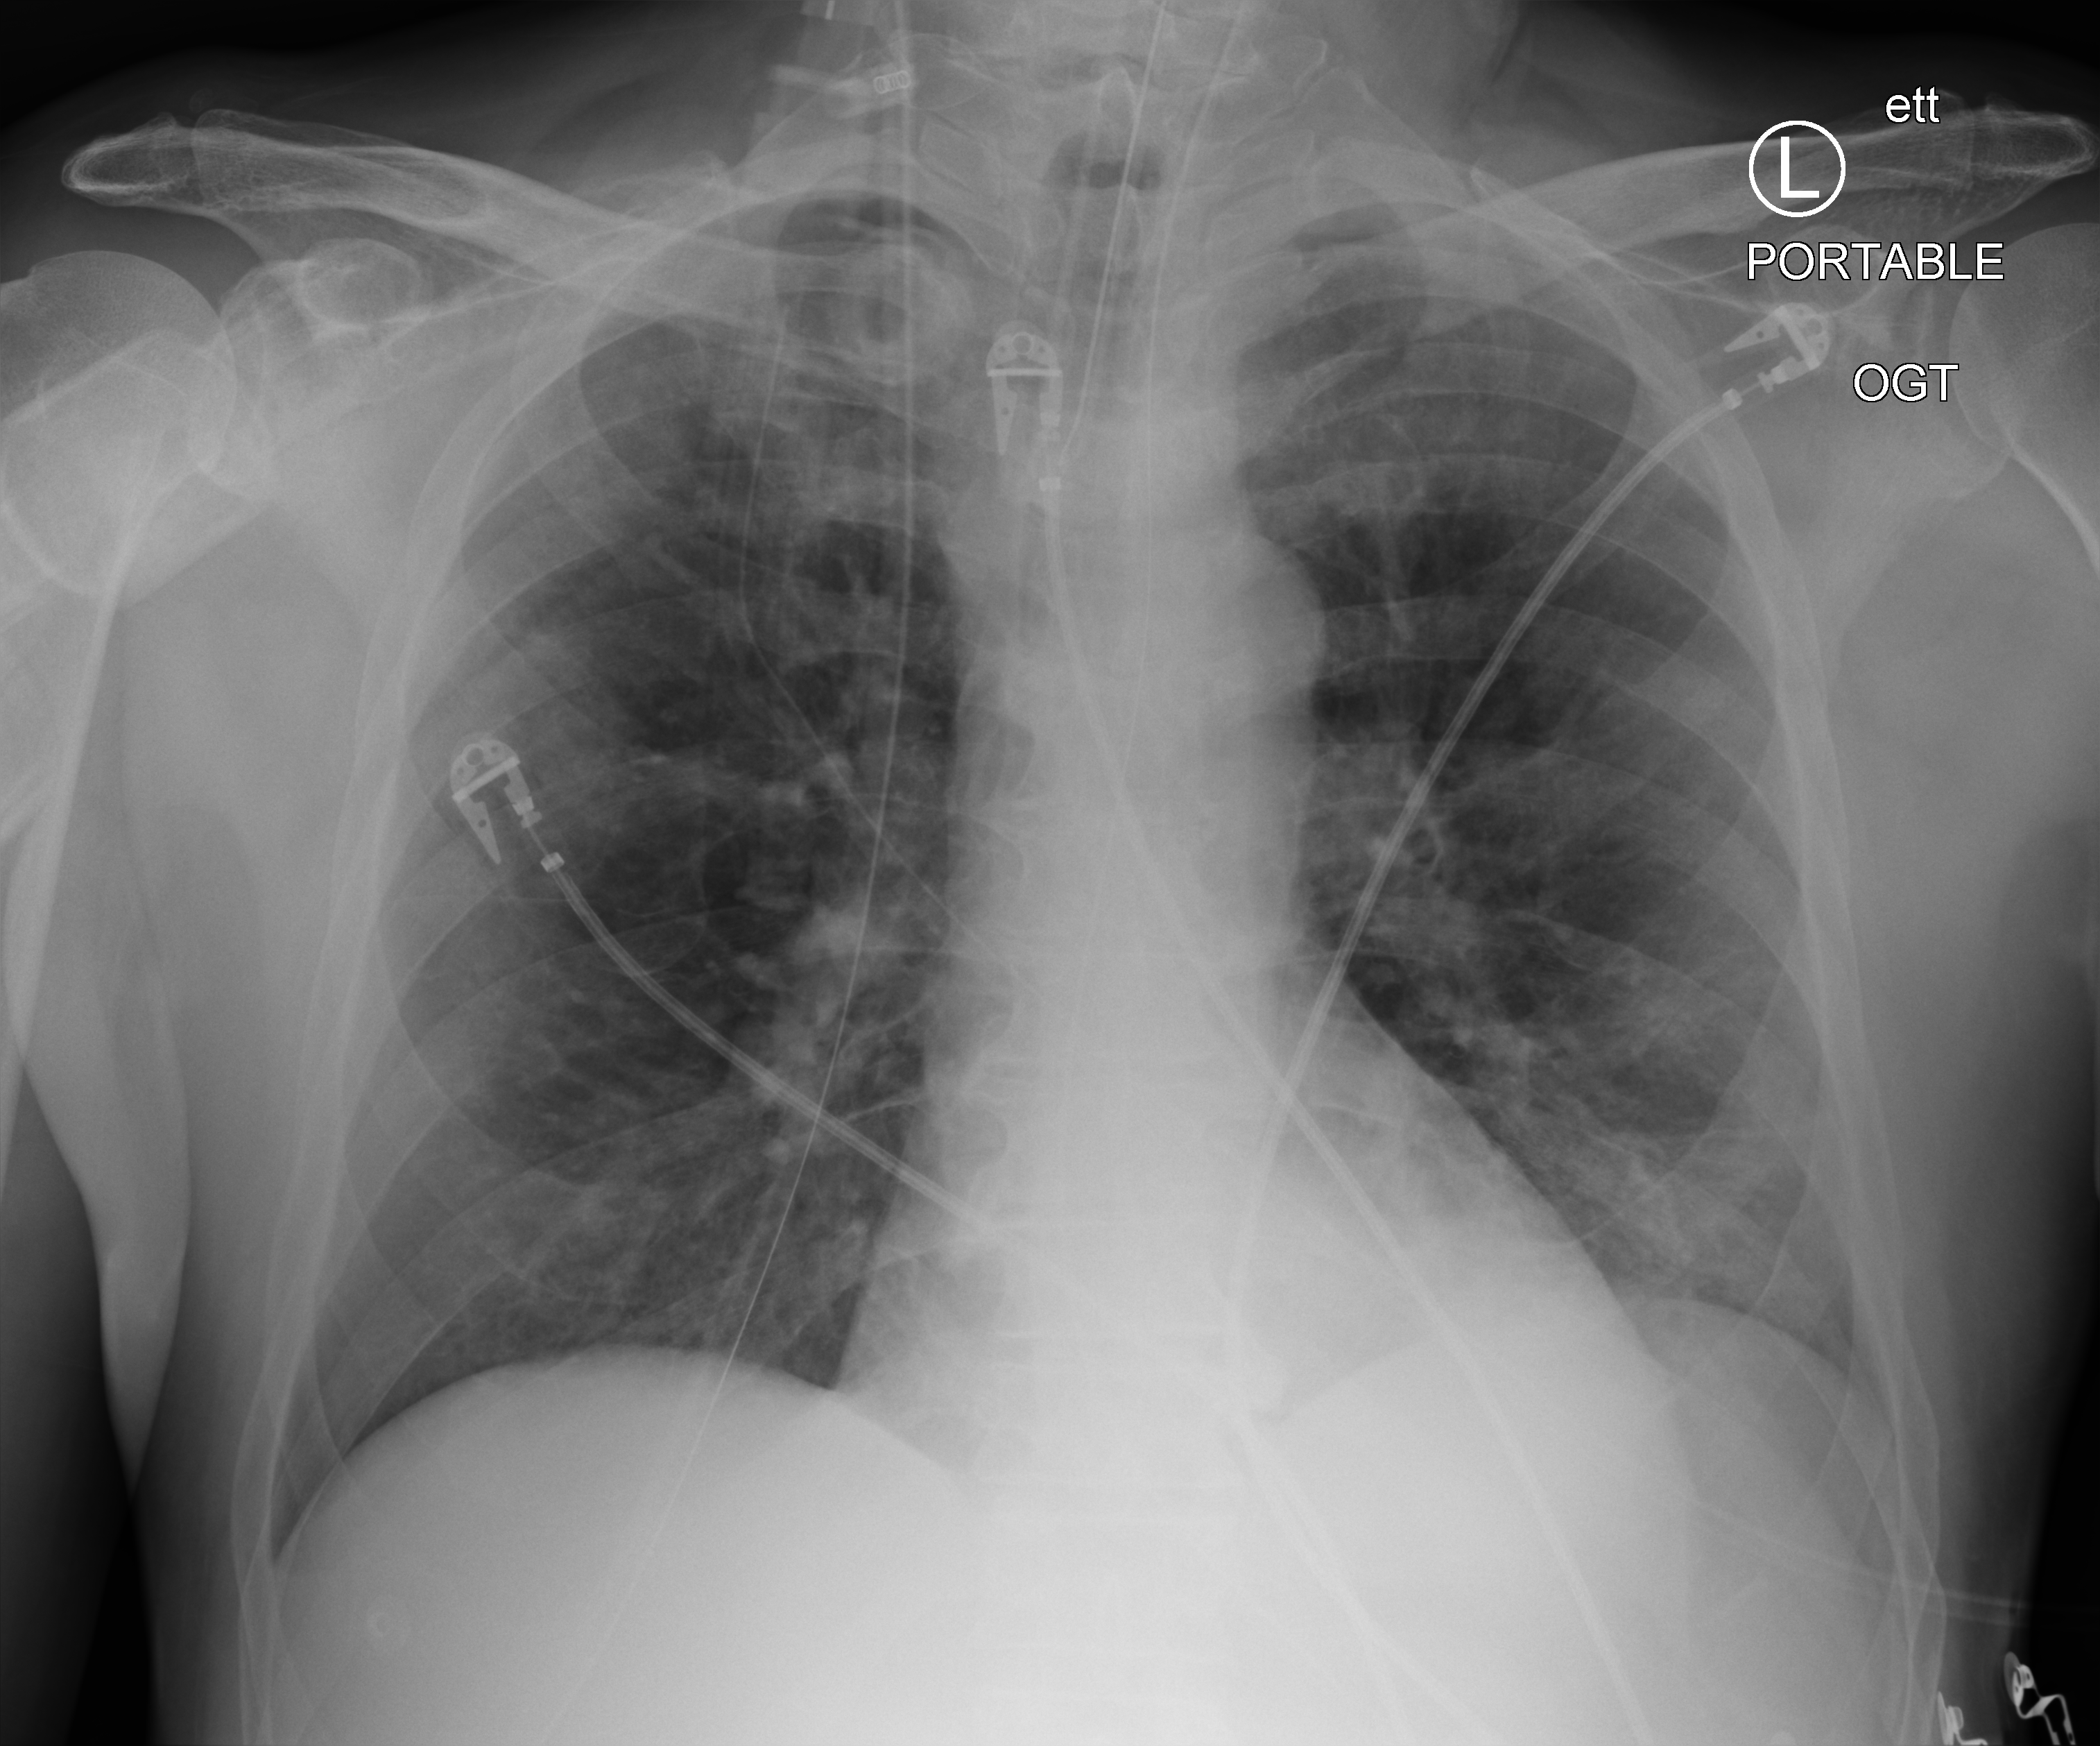
Bedside chest radiograph (computed radiography). Male patient hospitalised with COVID-19, age 60–74 years.
From the hospital-stay record, not from the radiograph (when in the stay this image was taken is not recorded):
- mechanically ventilated during this hospital stay: yes
- length of hospital stay: 35 days
- chronic kidney disease (admission record): no